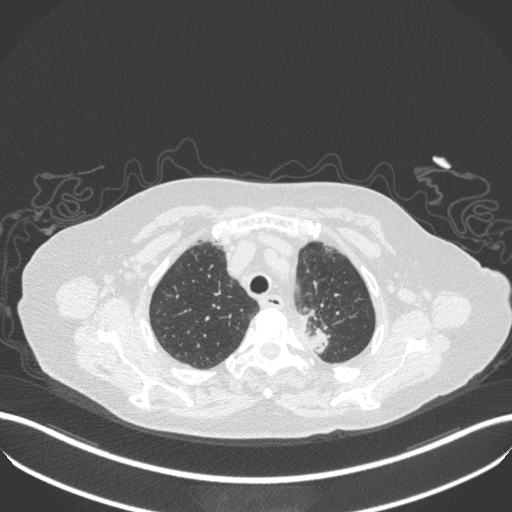
Chest CT, one axial slice; slice 279 of 353 in the series (ordered by position); reconstruction kernel B31f; 100 kVp; lung window (W 1500 / L -600 HU); 1 mm slice thickness; 512 × 512 image matrix, field of view 400 × 400 mm. Patient: female, 81 years. From the clinical record (not read from this slice): clinical TNM (as recorded): T2a N0 M0.
Structures marked on this image (bounding box drawn by a radiologist):
- lung tumour (recorded histology: adenocarcinoma): box from (x=282, y=304) to (x=338, y=356) px